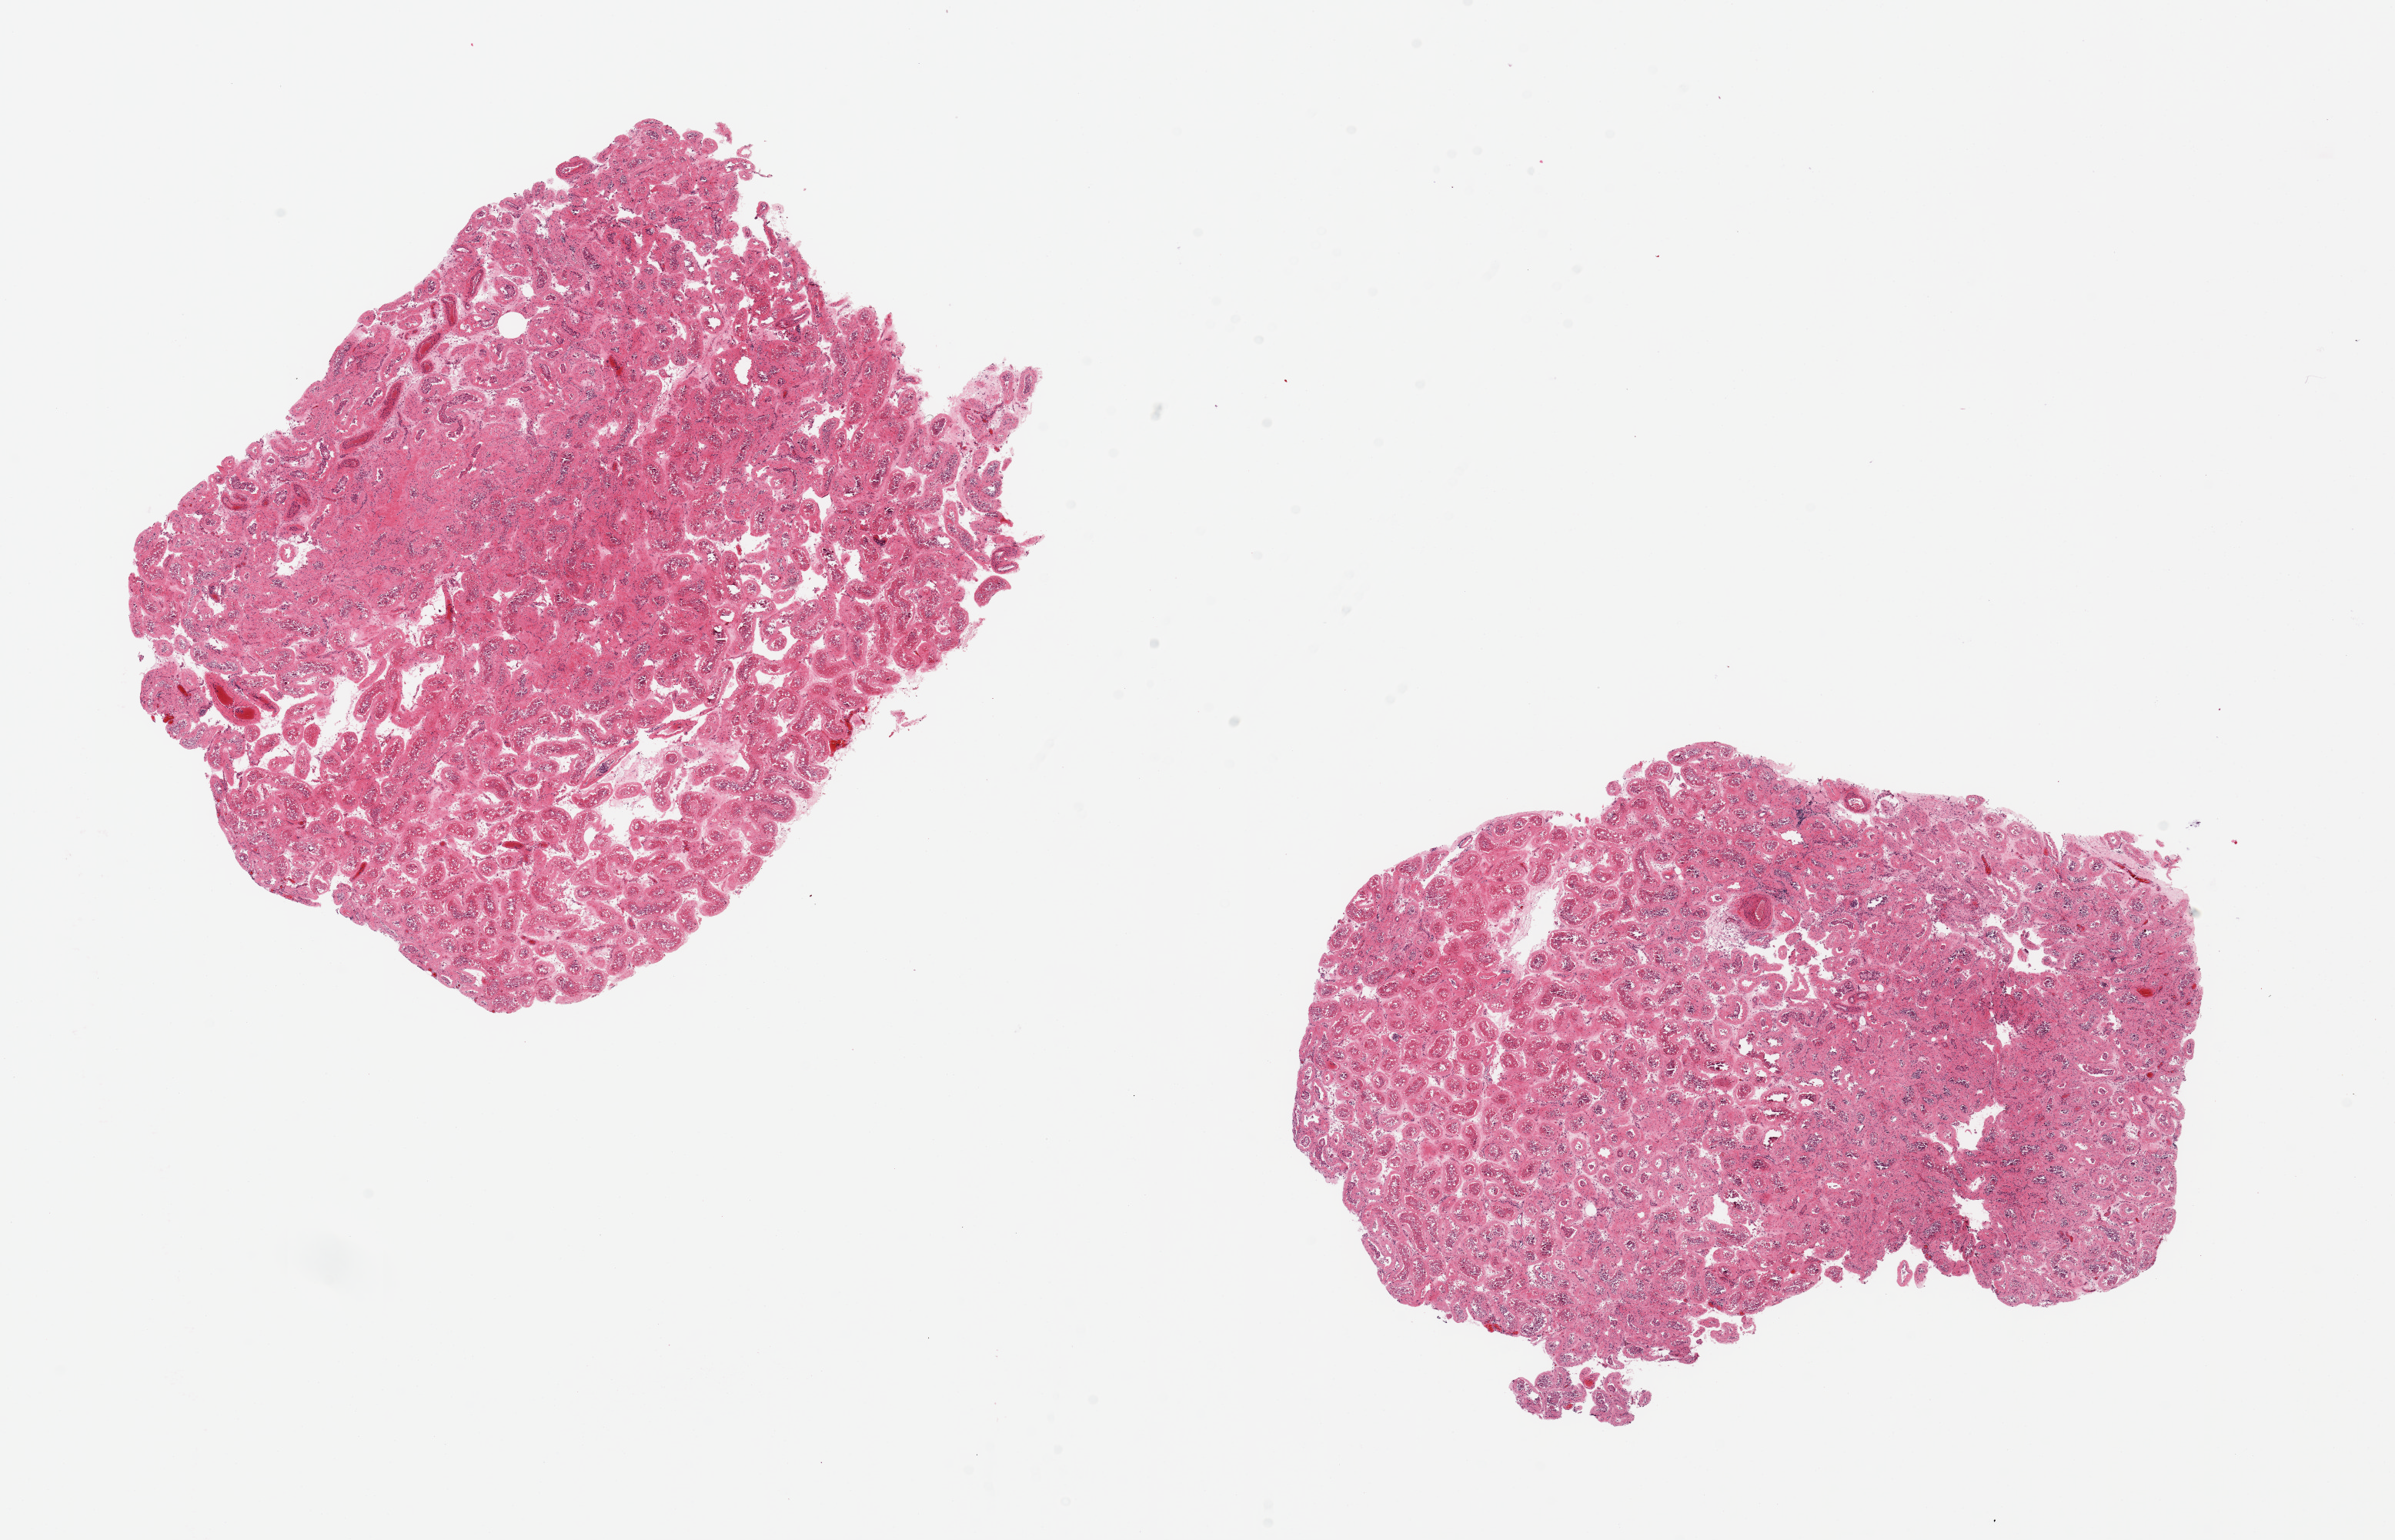
Whole-slide image, H&E stain, brightfield — a low-resolution overview of the entire scanned area, about 24.6 x 15.8 mm; PAXgene-fixed, paraffin-embedded tissue; sampled site (target tissue): testis; tissue donor sample. Donor sex: male.
Review note (as recorded): 2 pieces, too badly autolyzed to assess, ~9x7mm.